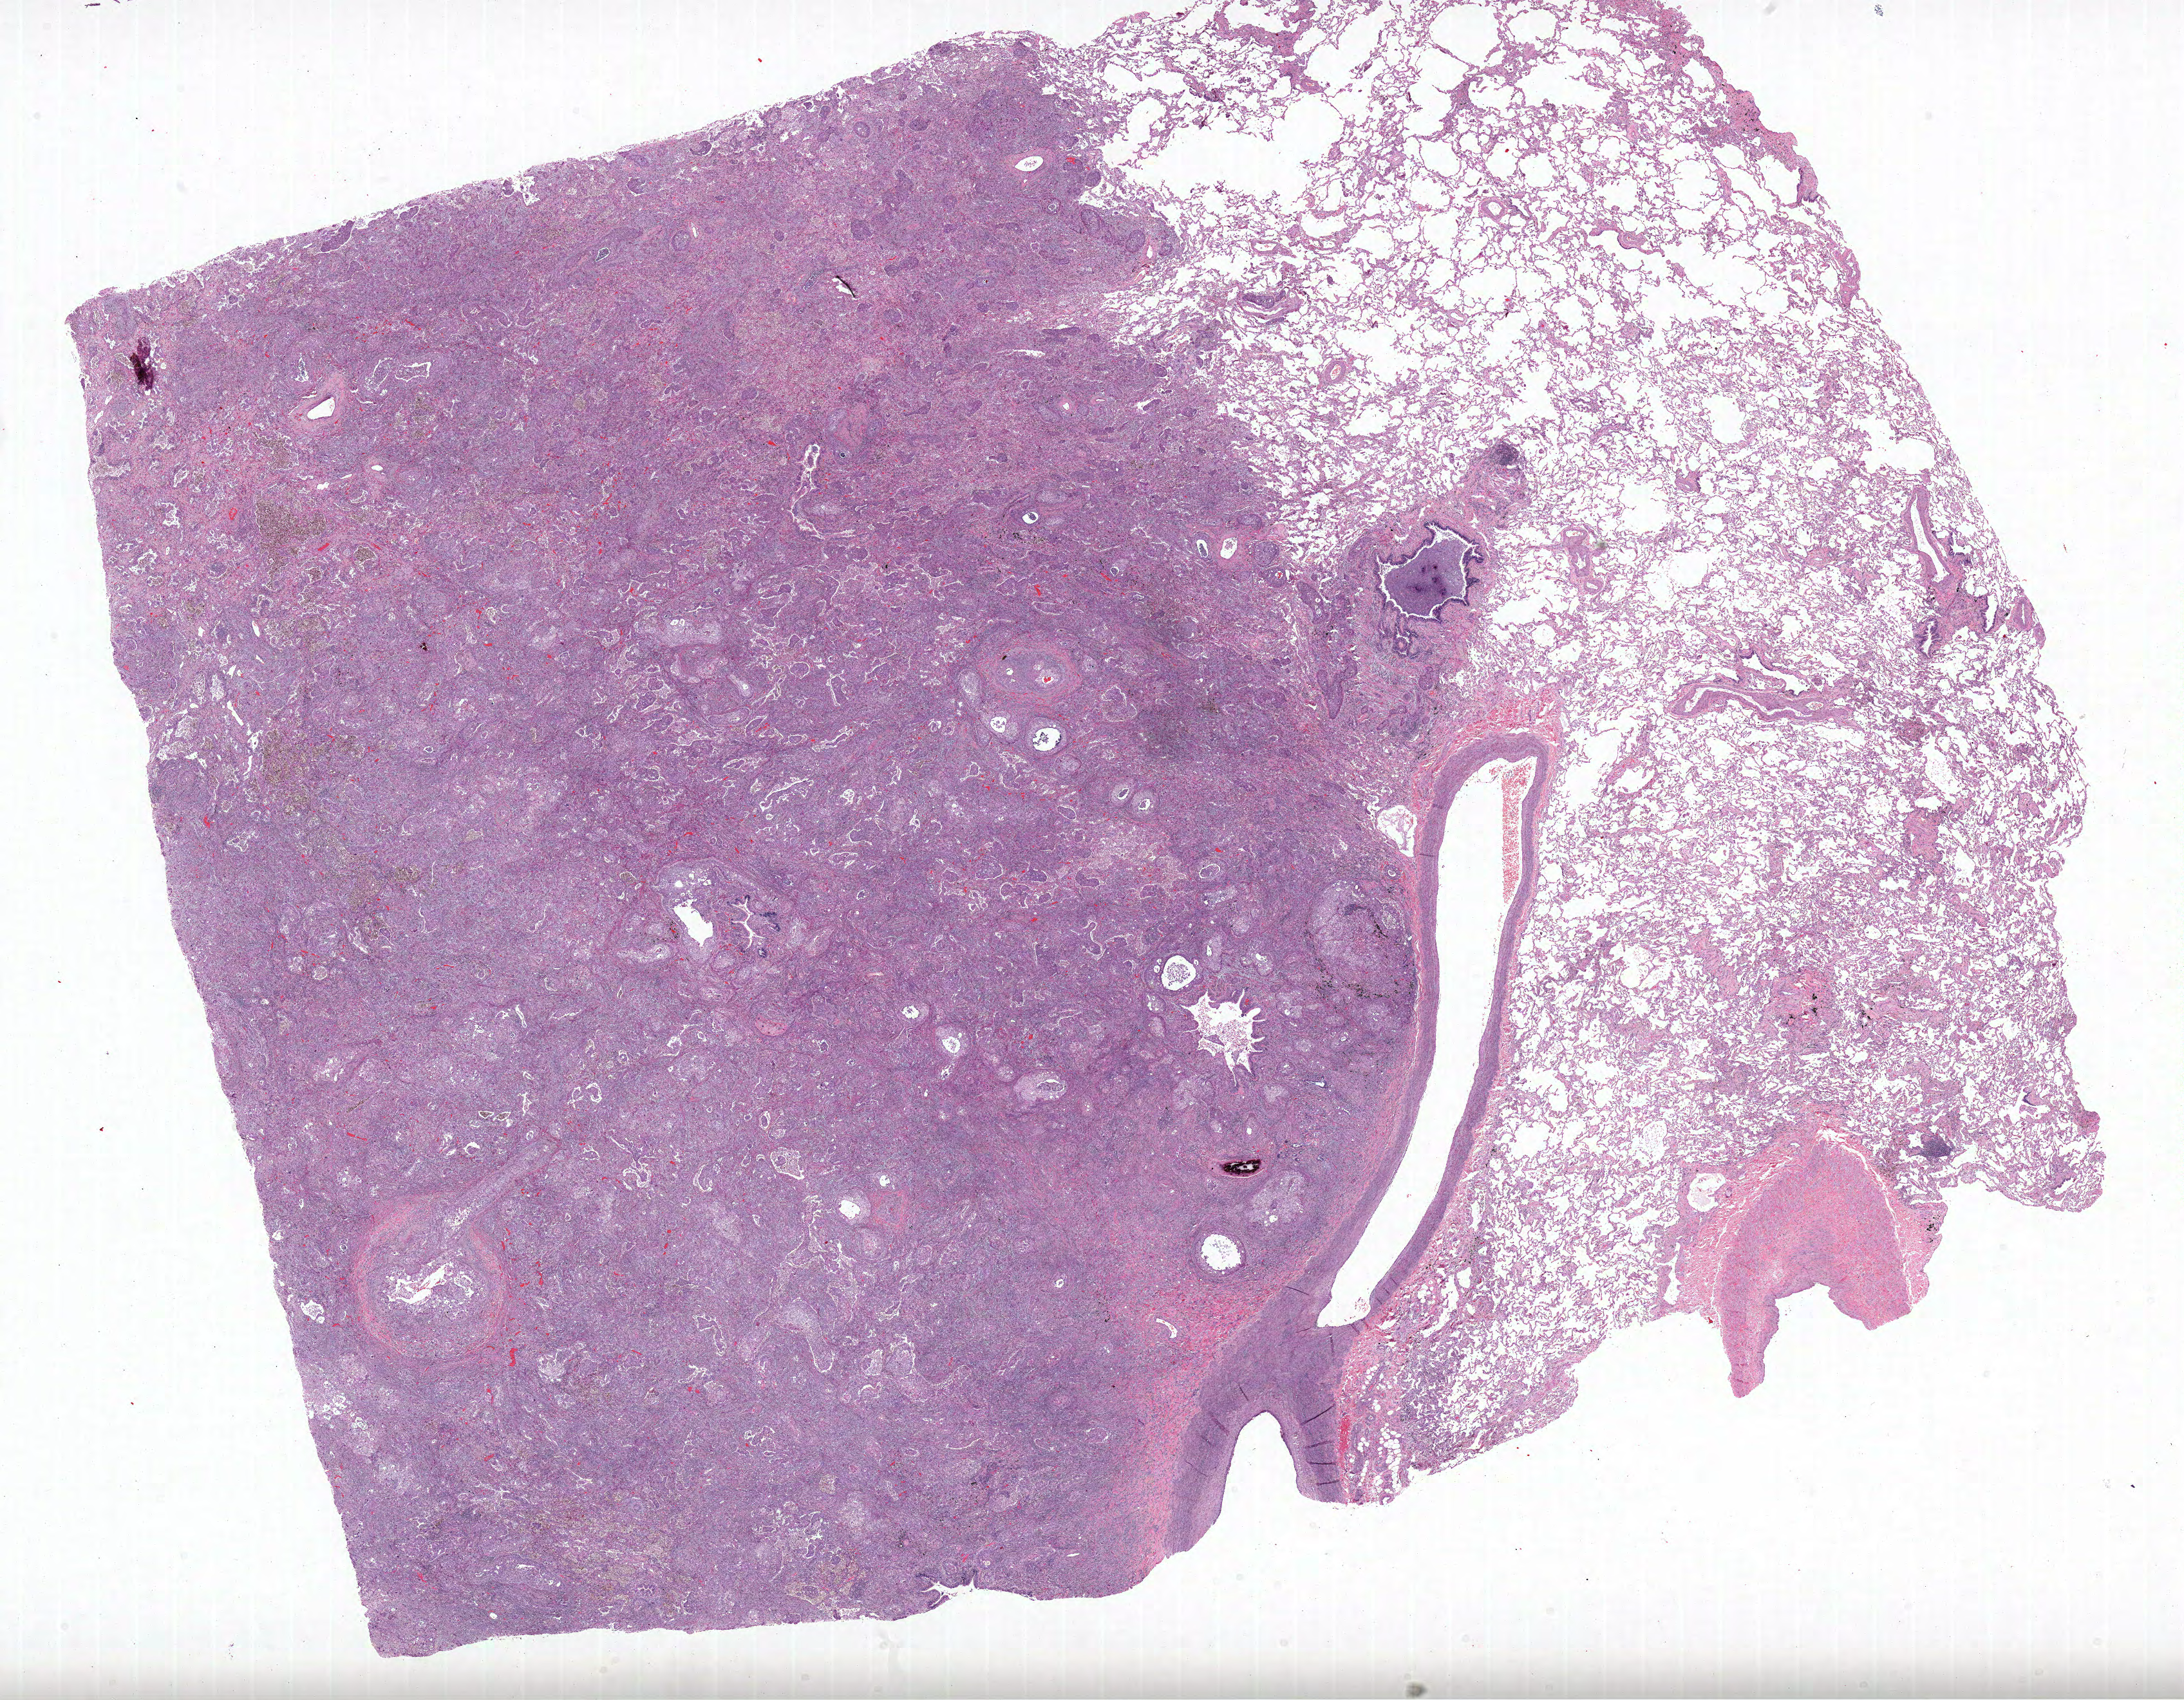
Digitized H&E-stained tissue section (whole slide) — low-resolution overview of the scanned area, about 27.4 x 21.3 mm (from a 20x scan). Formalin-fixed paraffin-embedded (FFPE) diagnostic section. Sample: primary tumour, lung. Male patient; age at initial diagnosis 76 years.
Diagnosis: Squamous cell carcinoma, NOS (upper lobe, lung). Laterality: right. AJCC pathologic stage: IIA.